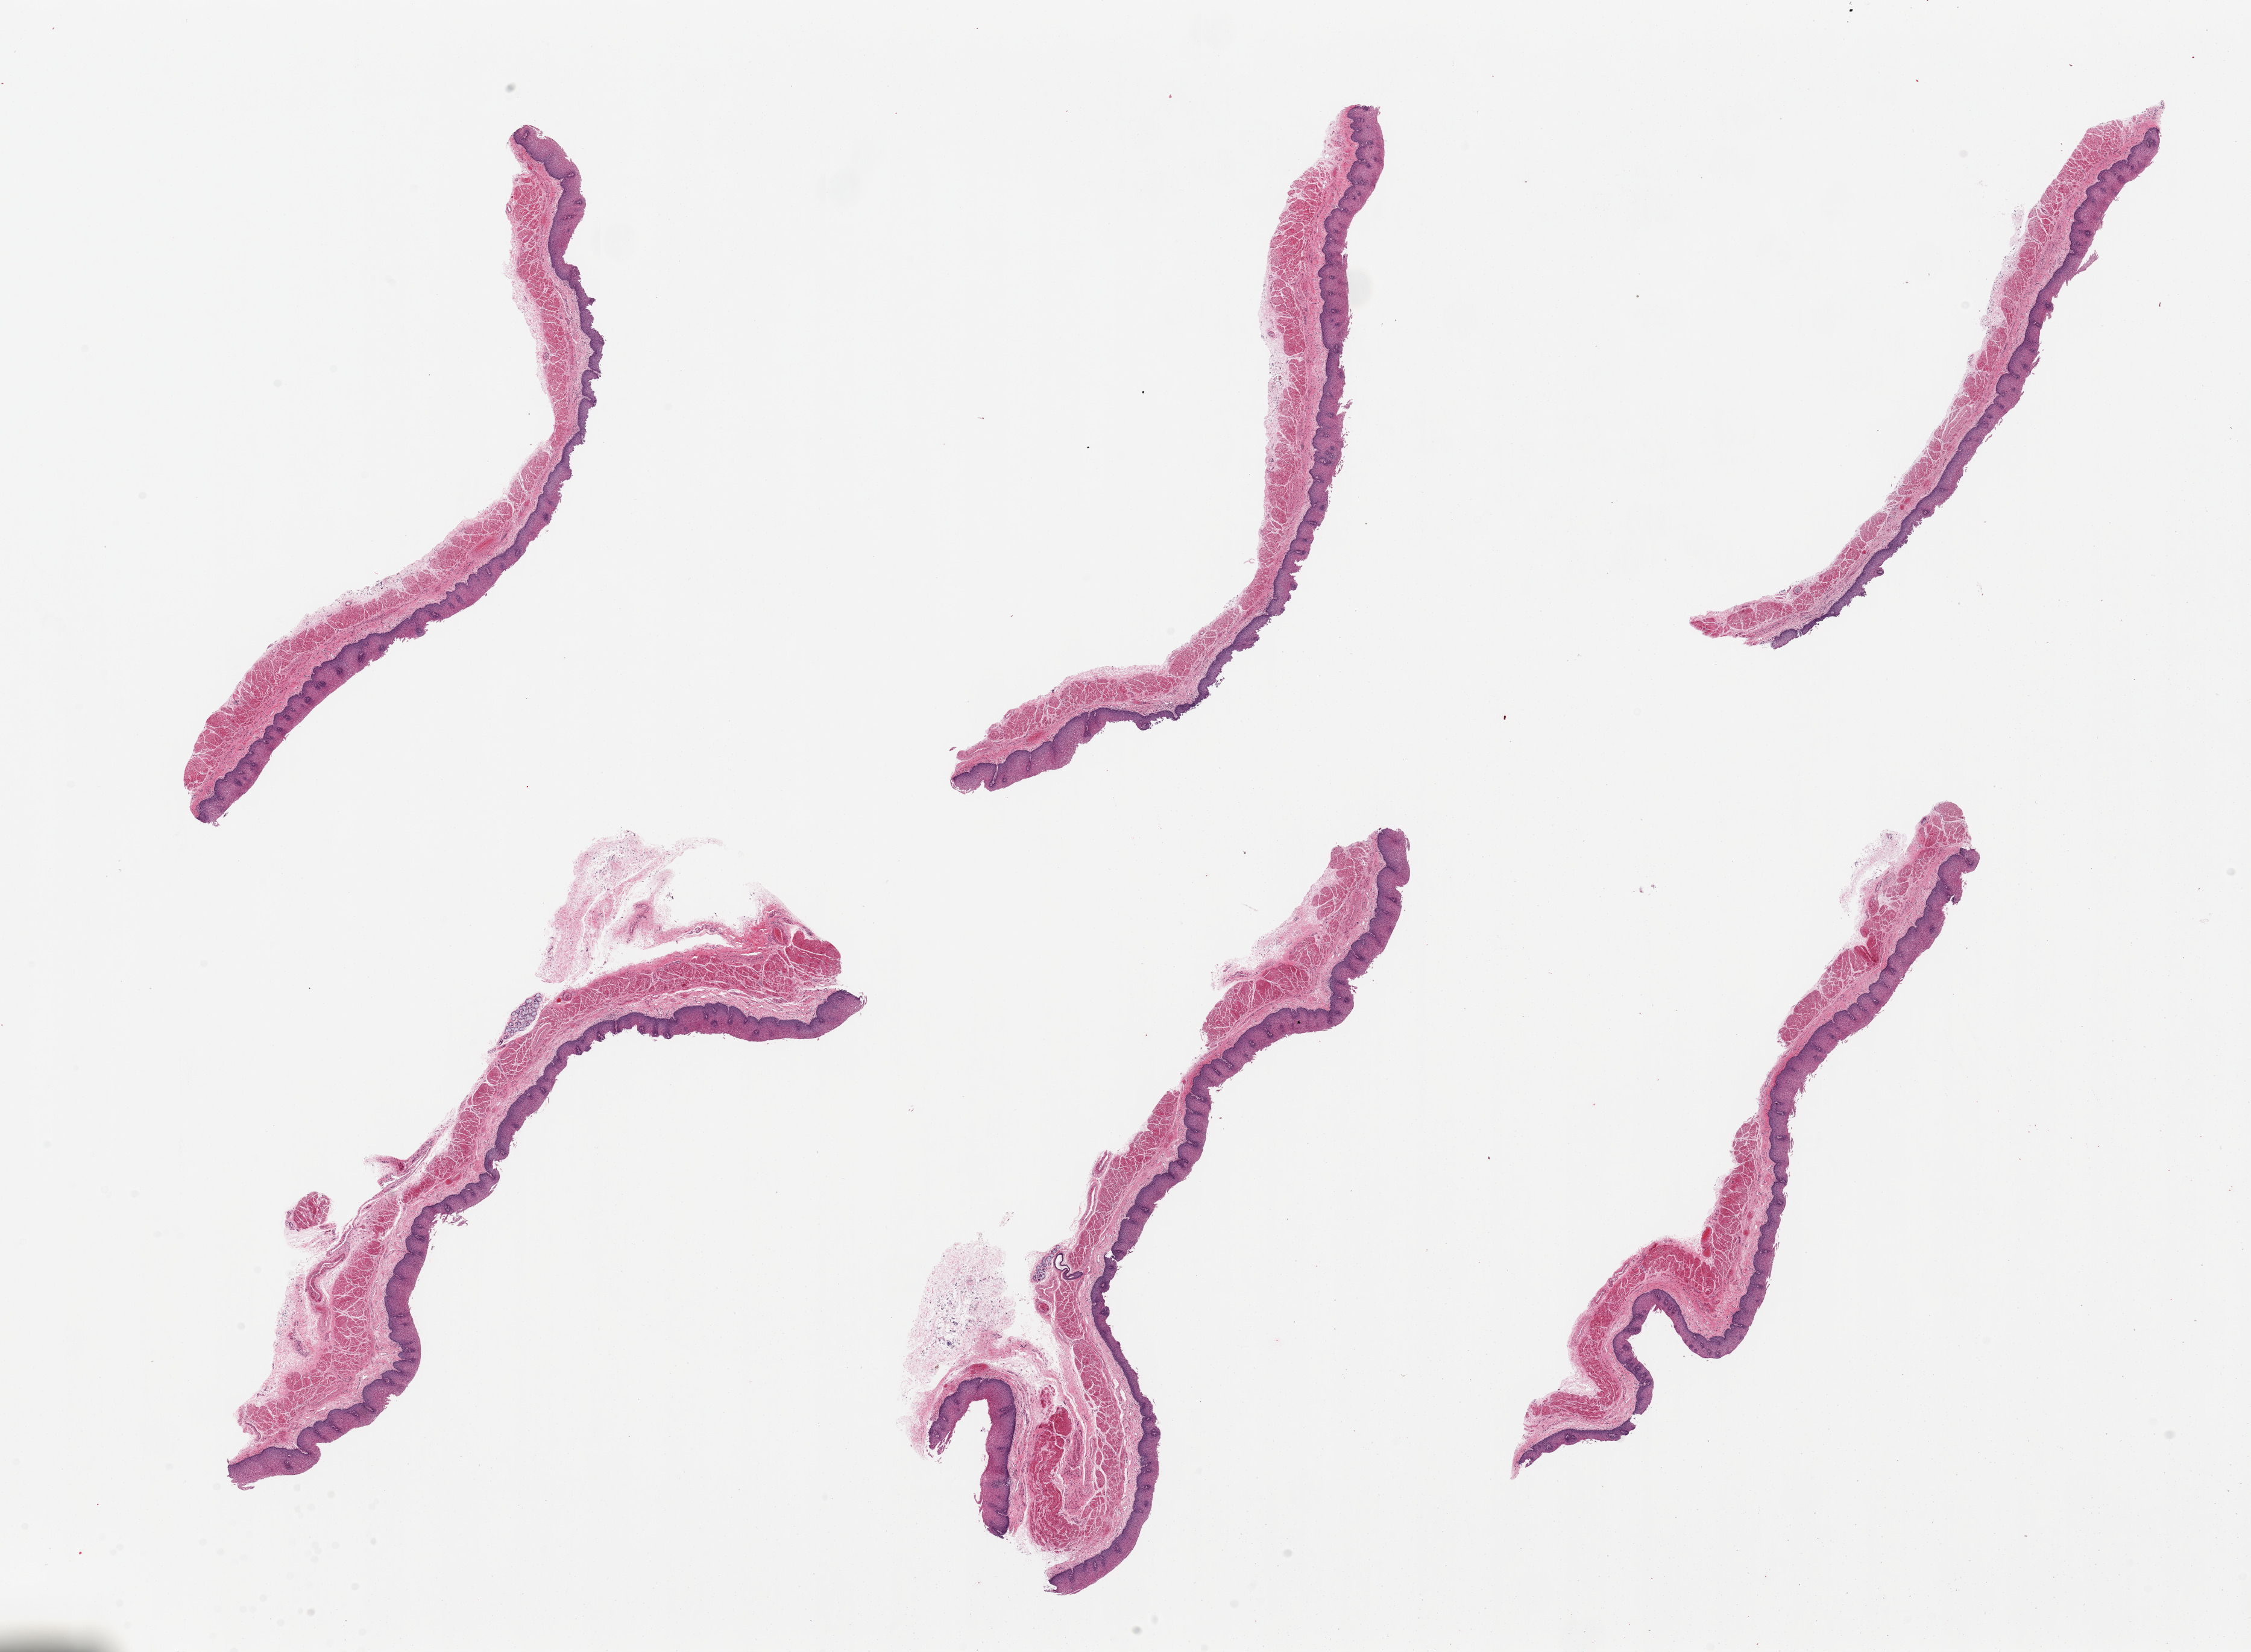
Hematoxylin and eosin (H&E) whole-slide image, brightfield — shown as a low-resolution overview of the whole scanned area (about 29.5 x 21.7 mm, acquisition: 20x scan), PAXgene-fixed paraffin-embedded (PFPE) section, target tissue: esophageal mucous membrane, donor tissue sample. Donor sex: female.
• review note (as recorded): 6 pieces, squamous mucosa is 40-60% thickness, ~250 microns